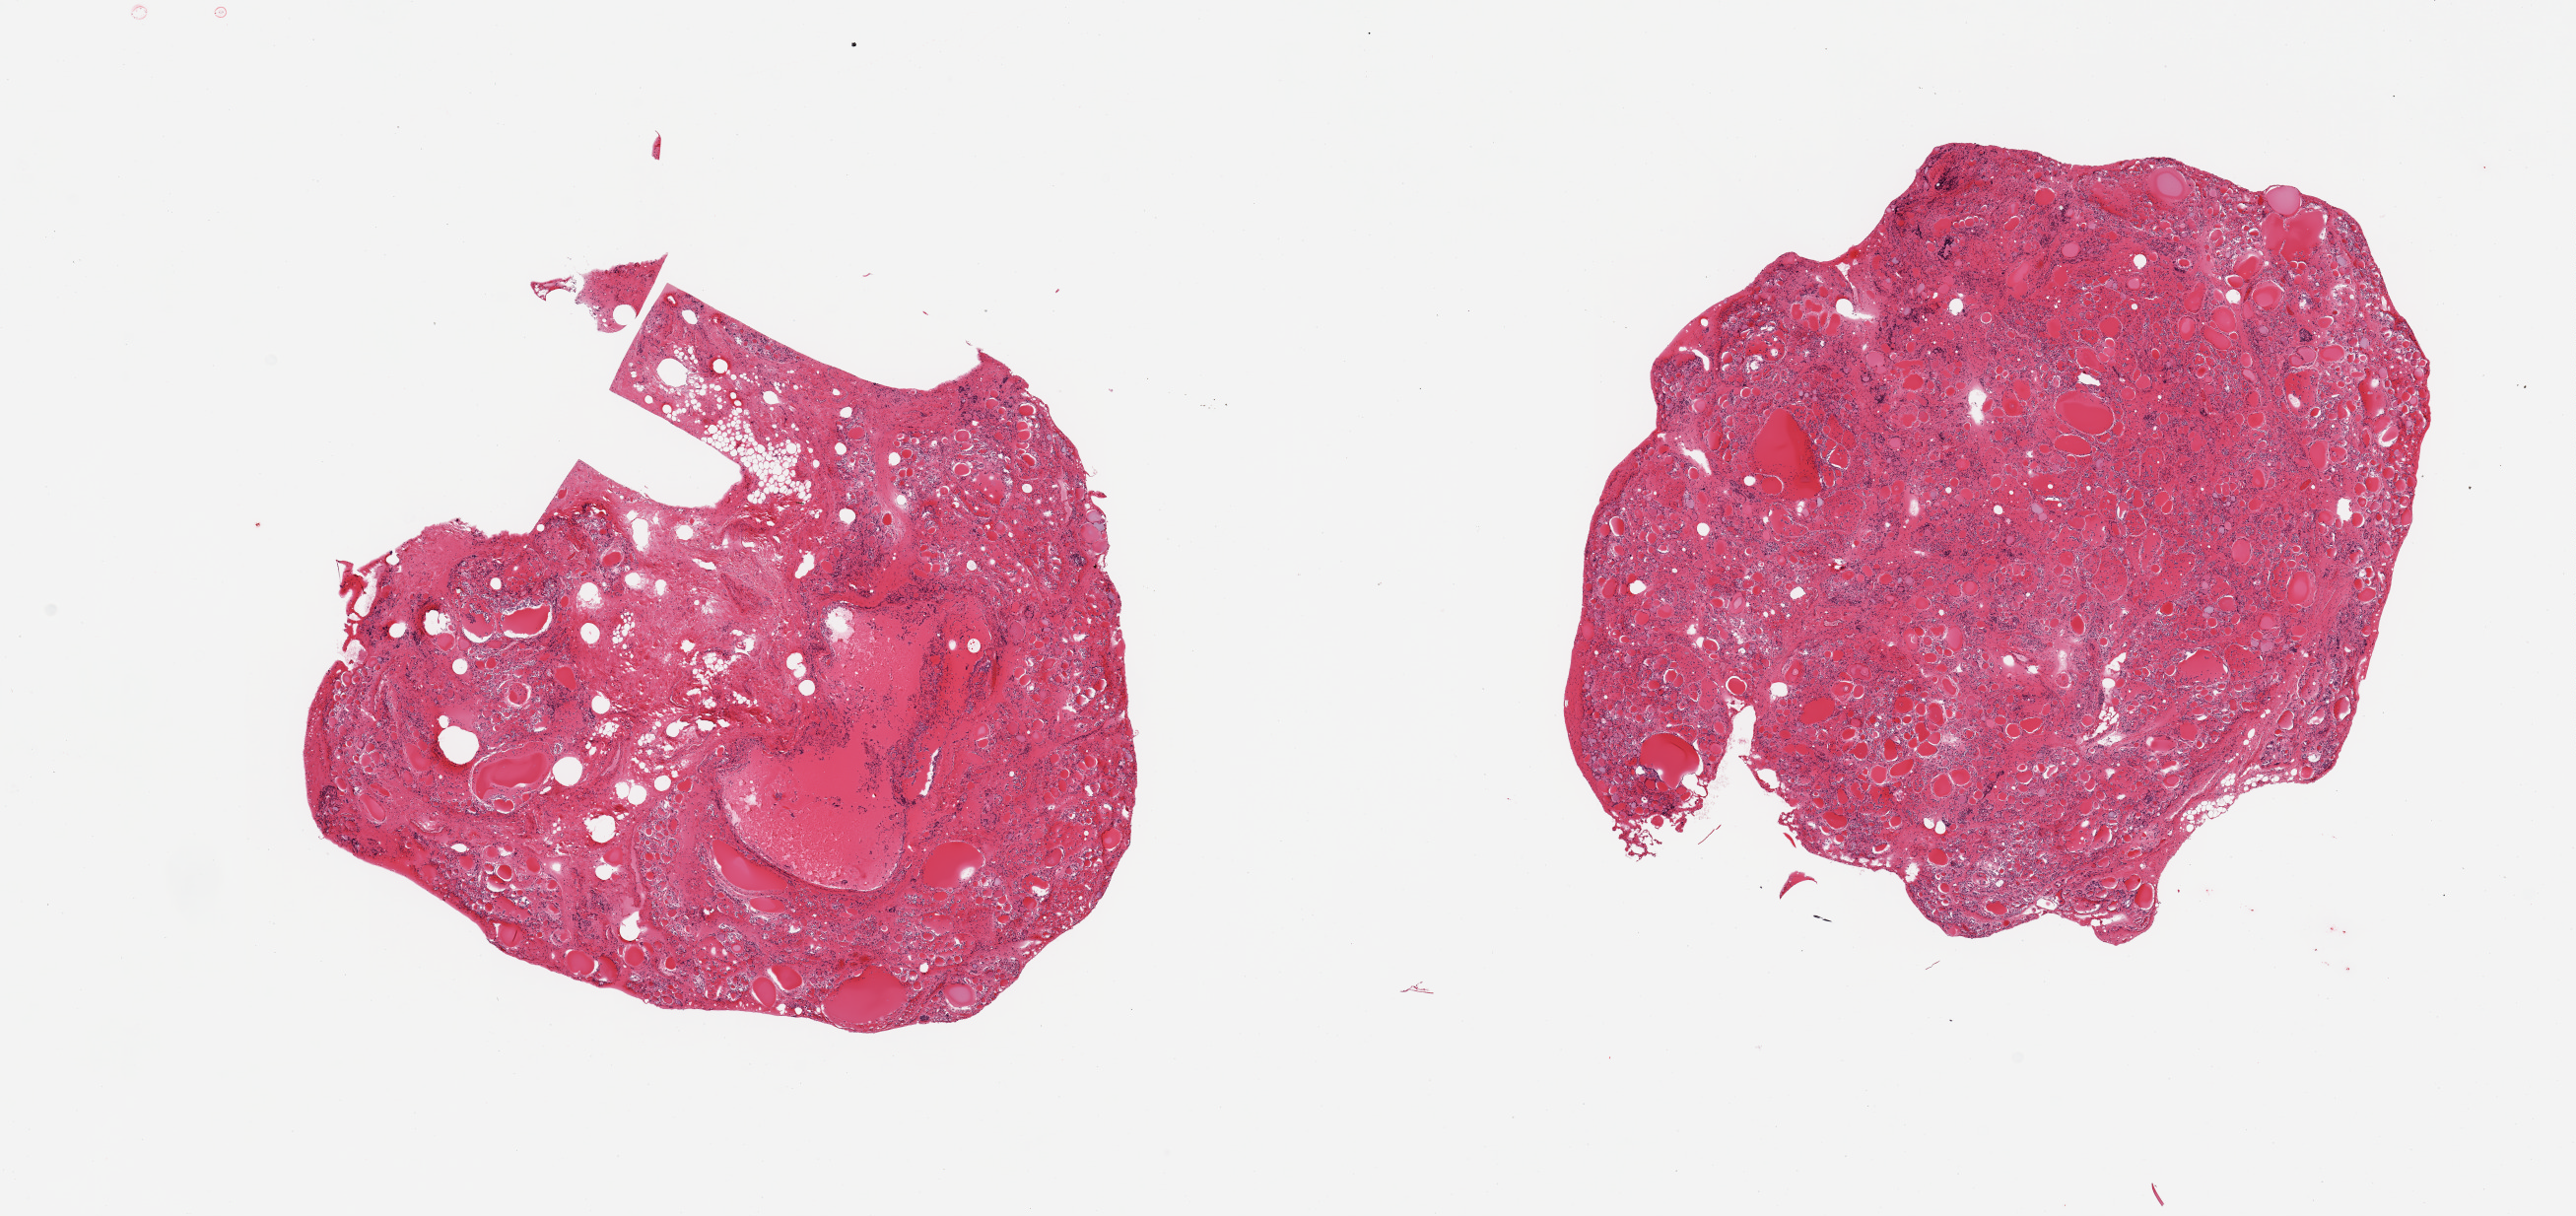
Whole-slide image, haematoxylin and eosin stain — low-resolution overview of the scanned area, about 20.7 x 9.8 mm; PAXgene-fixed paraffin-embedded (PFPE) section; sampled site (target tissue): thyroid; tissue donor sample.
- pathologist's review note for this sample: 2 pieces; multinodular with some fibrosis, one piece includes portion of fat/fibrous tissue